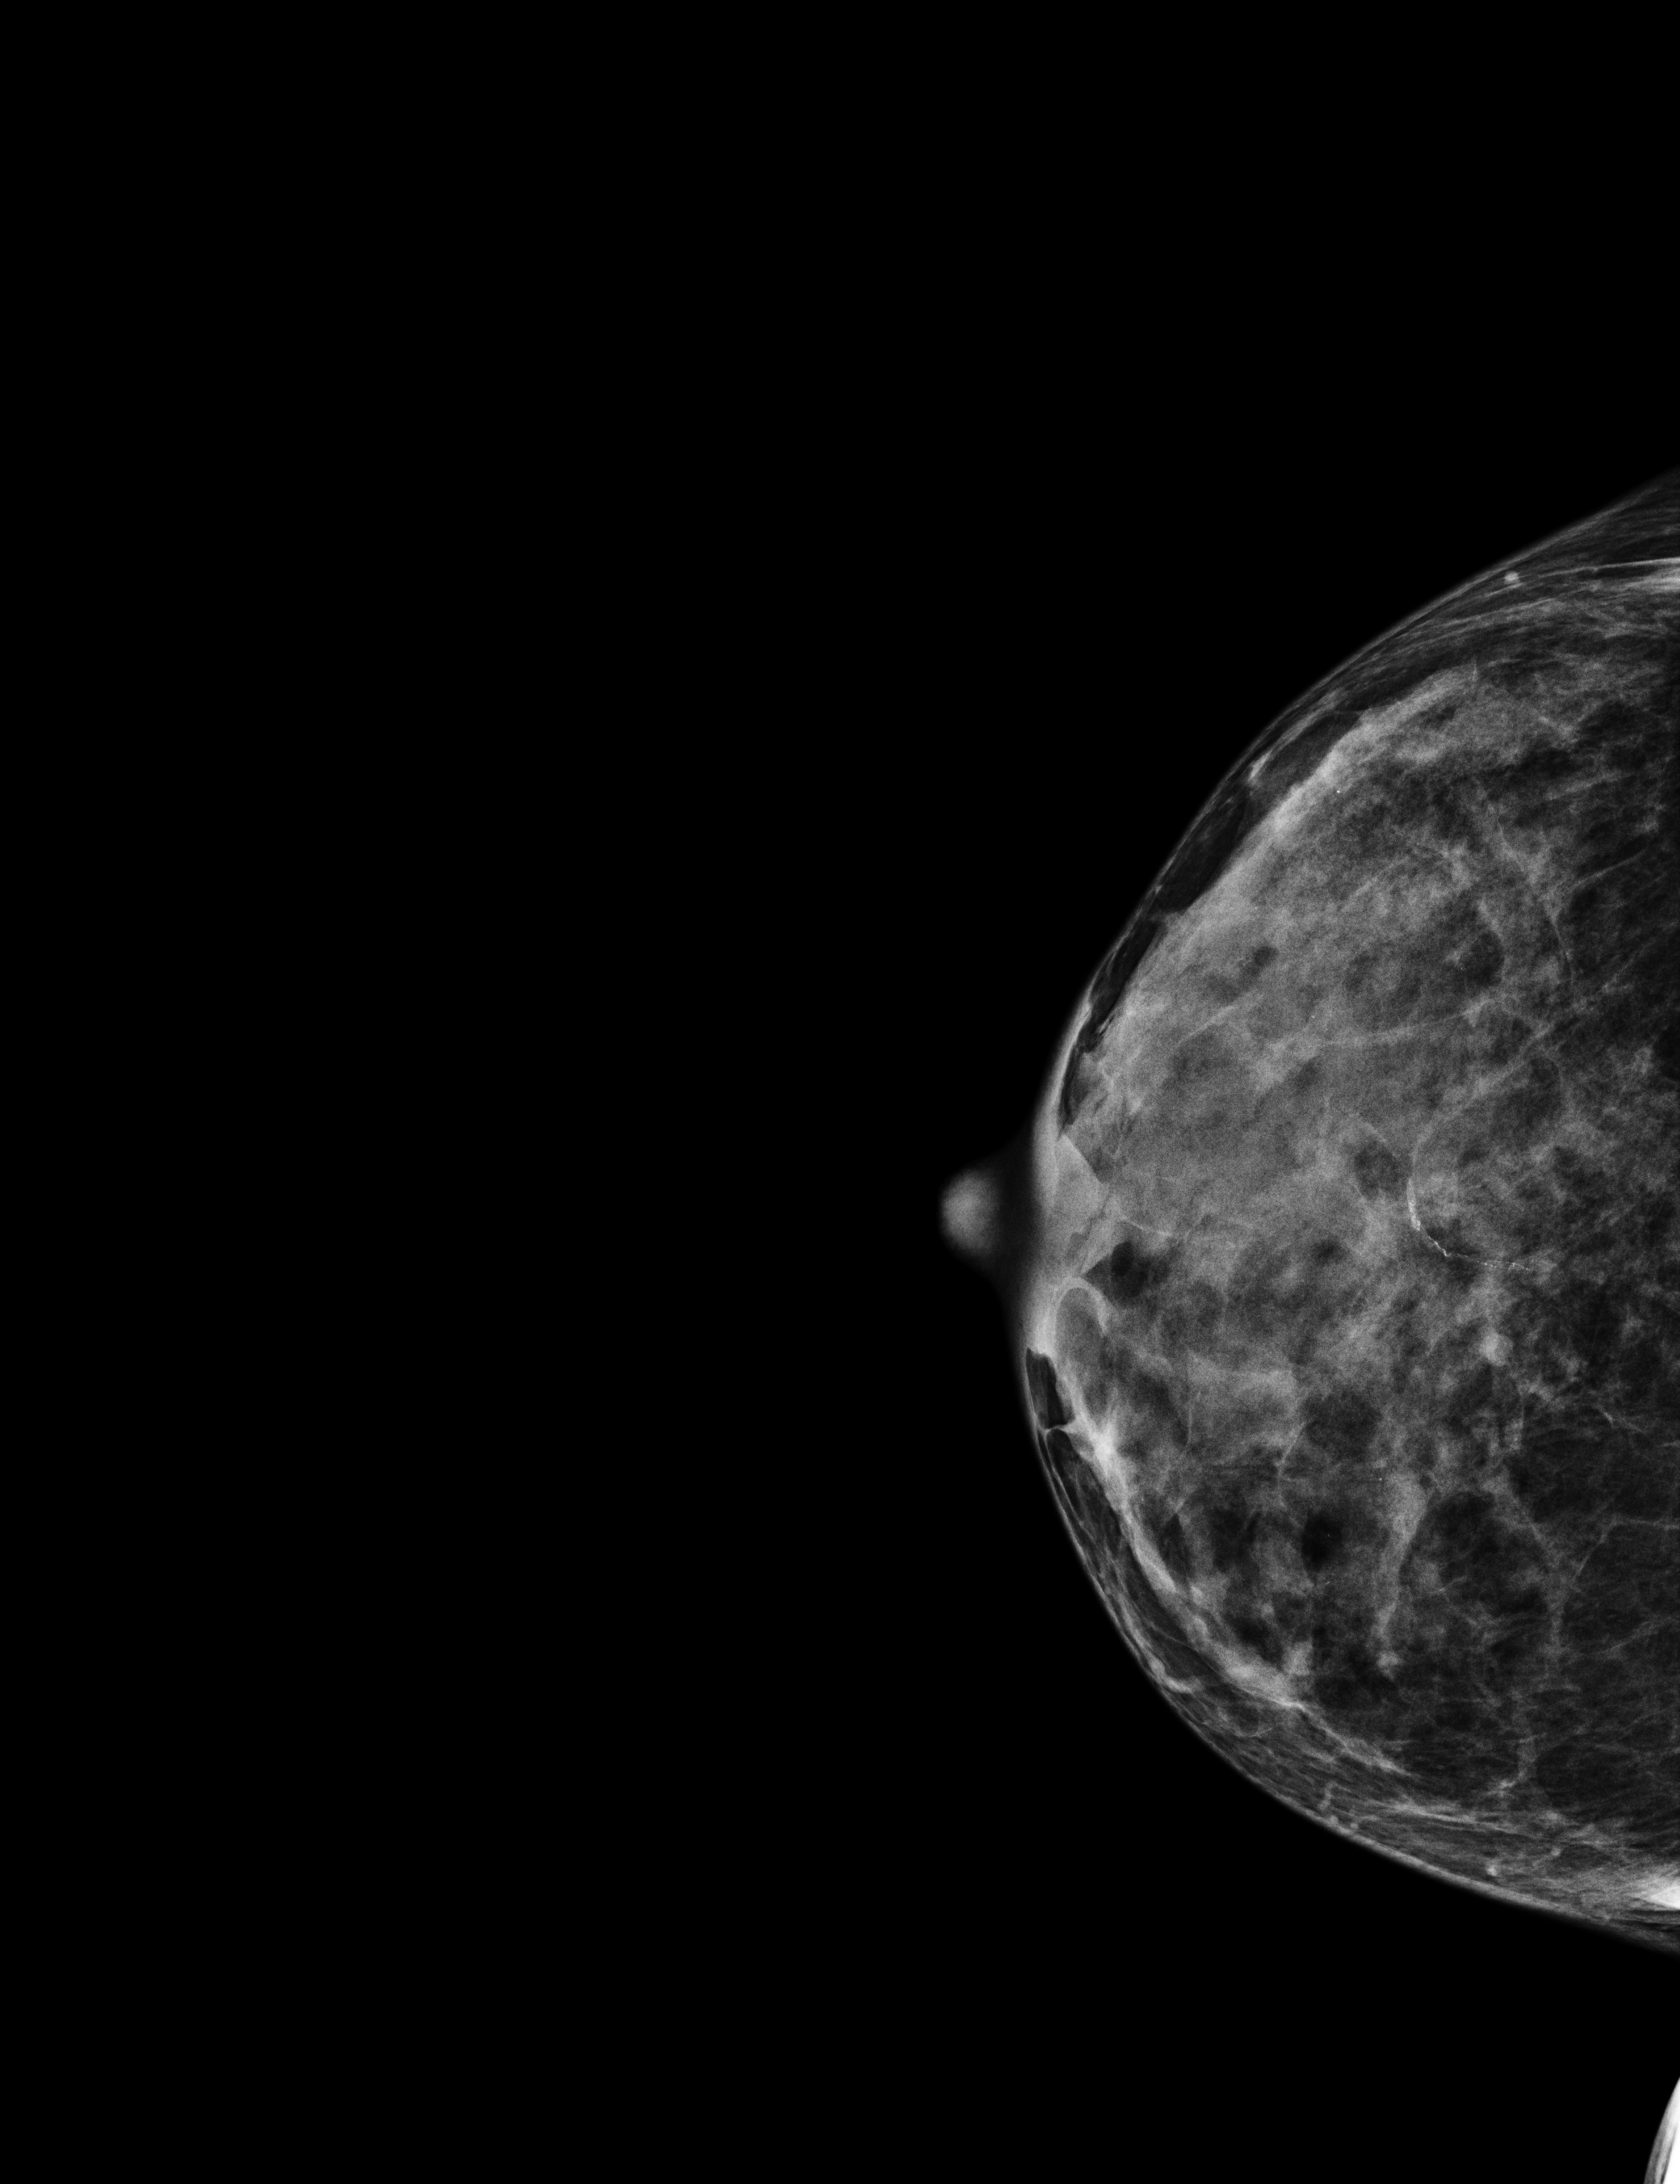
Screening examination; compressed breast thickness 24 mm. Female patient, age 59 years.
Image type: full-field digital mammogram. Breast: right. Projection: CC view.